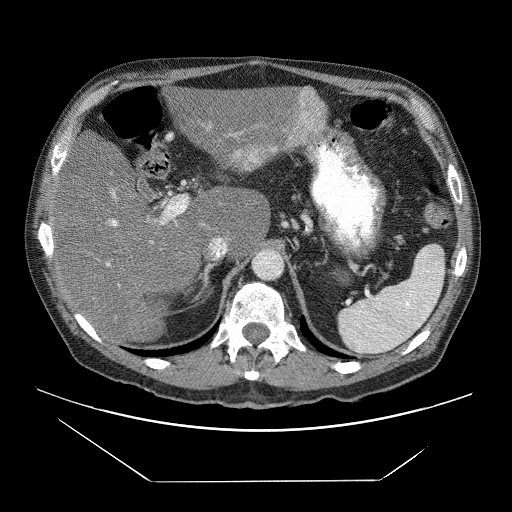
Contrast-enhanced abdominal CT (liver protocol), one axial slice. Position 41 of 83 along the scan axis. Reconstruction kernel STANDARD. 120 kVp. Soft-tissue window (W 400 / L 40 HU). 2.5 mm slice thickness. 512 × 512 image matrix, field of view 420 × 420 mm. From the clinical record (not read from this slice): diagnosis: hepatocellular carcinoma (patient treated with transarterial chemoembolisation; whether this scan precedes or follows treatment is not stated here); TNM stage (as recorded): Stage-IVB; Child-Pugh class: B; tumour differentiation: poorly differentiated; tumour nodularity: uninodular.
Annotated regions visible in this slice (semi-automatically segmented with operator editing):
- liver parenchyma outside the tumour (the mass and vessels are separate outlines, so this box may not span the whole liver): bounding box (x1, y1, x2, y2) in pixels: (50, 83, 326, 340)
- mass: (234, 90, 325, 170)
- liver vessels: (106, 126, 303, 266)